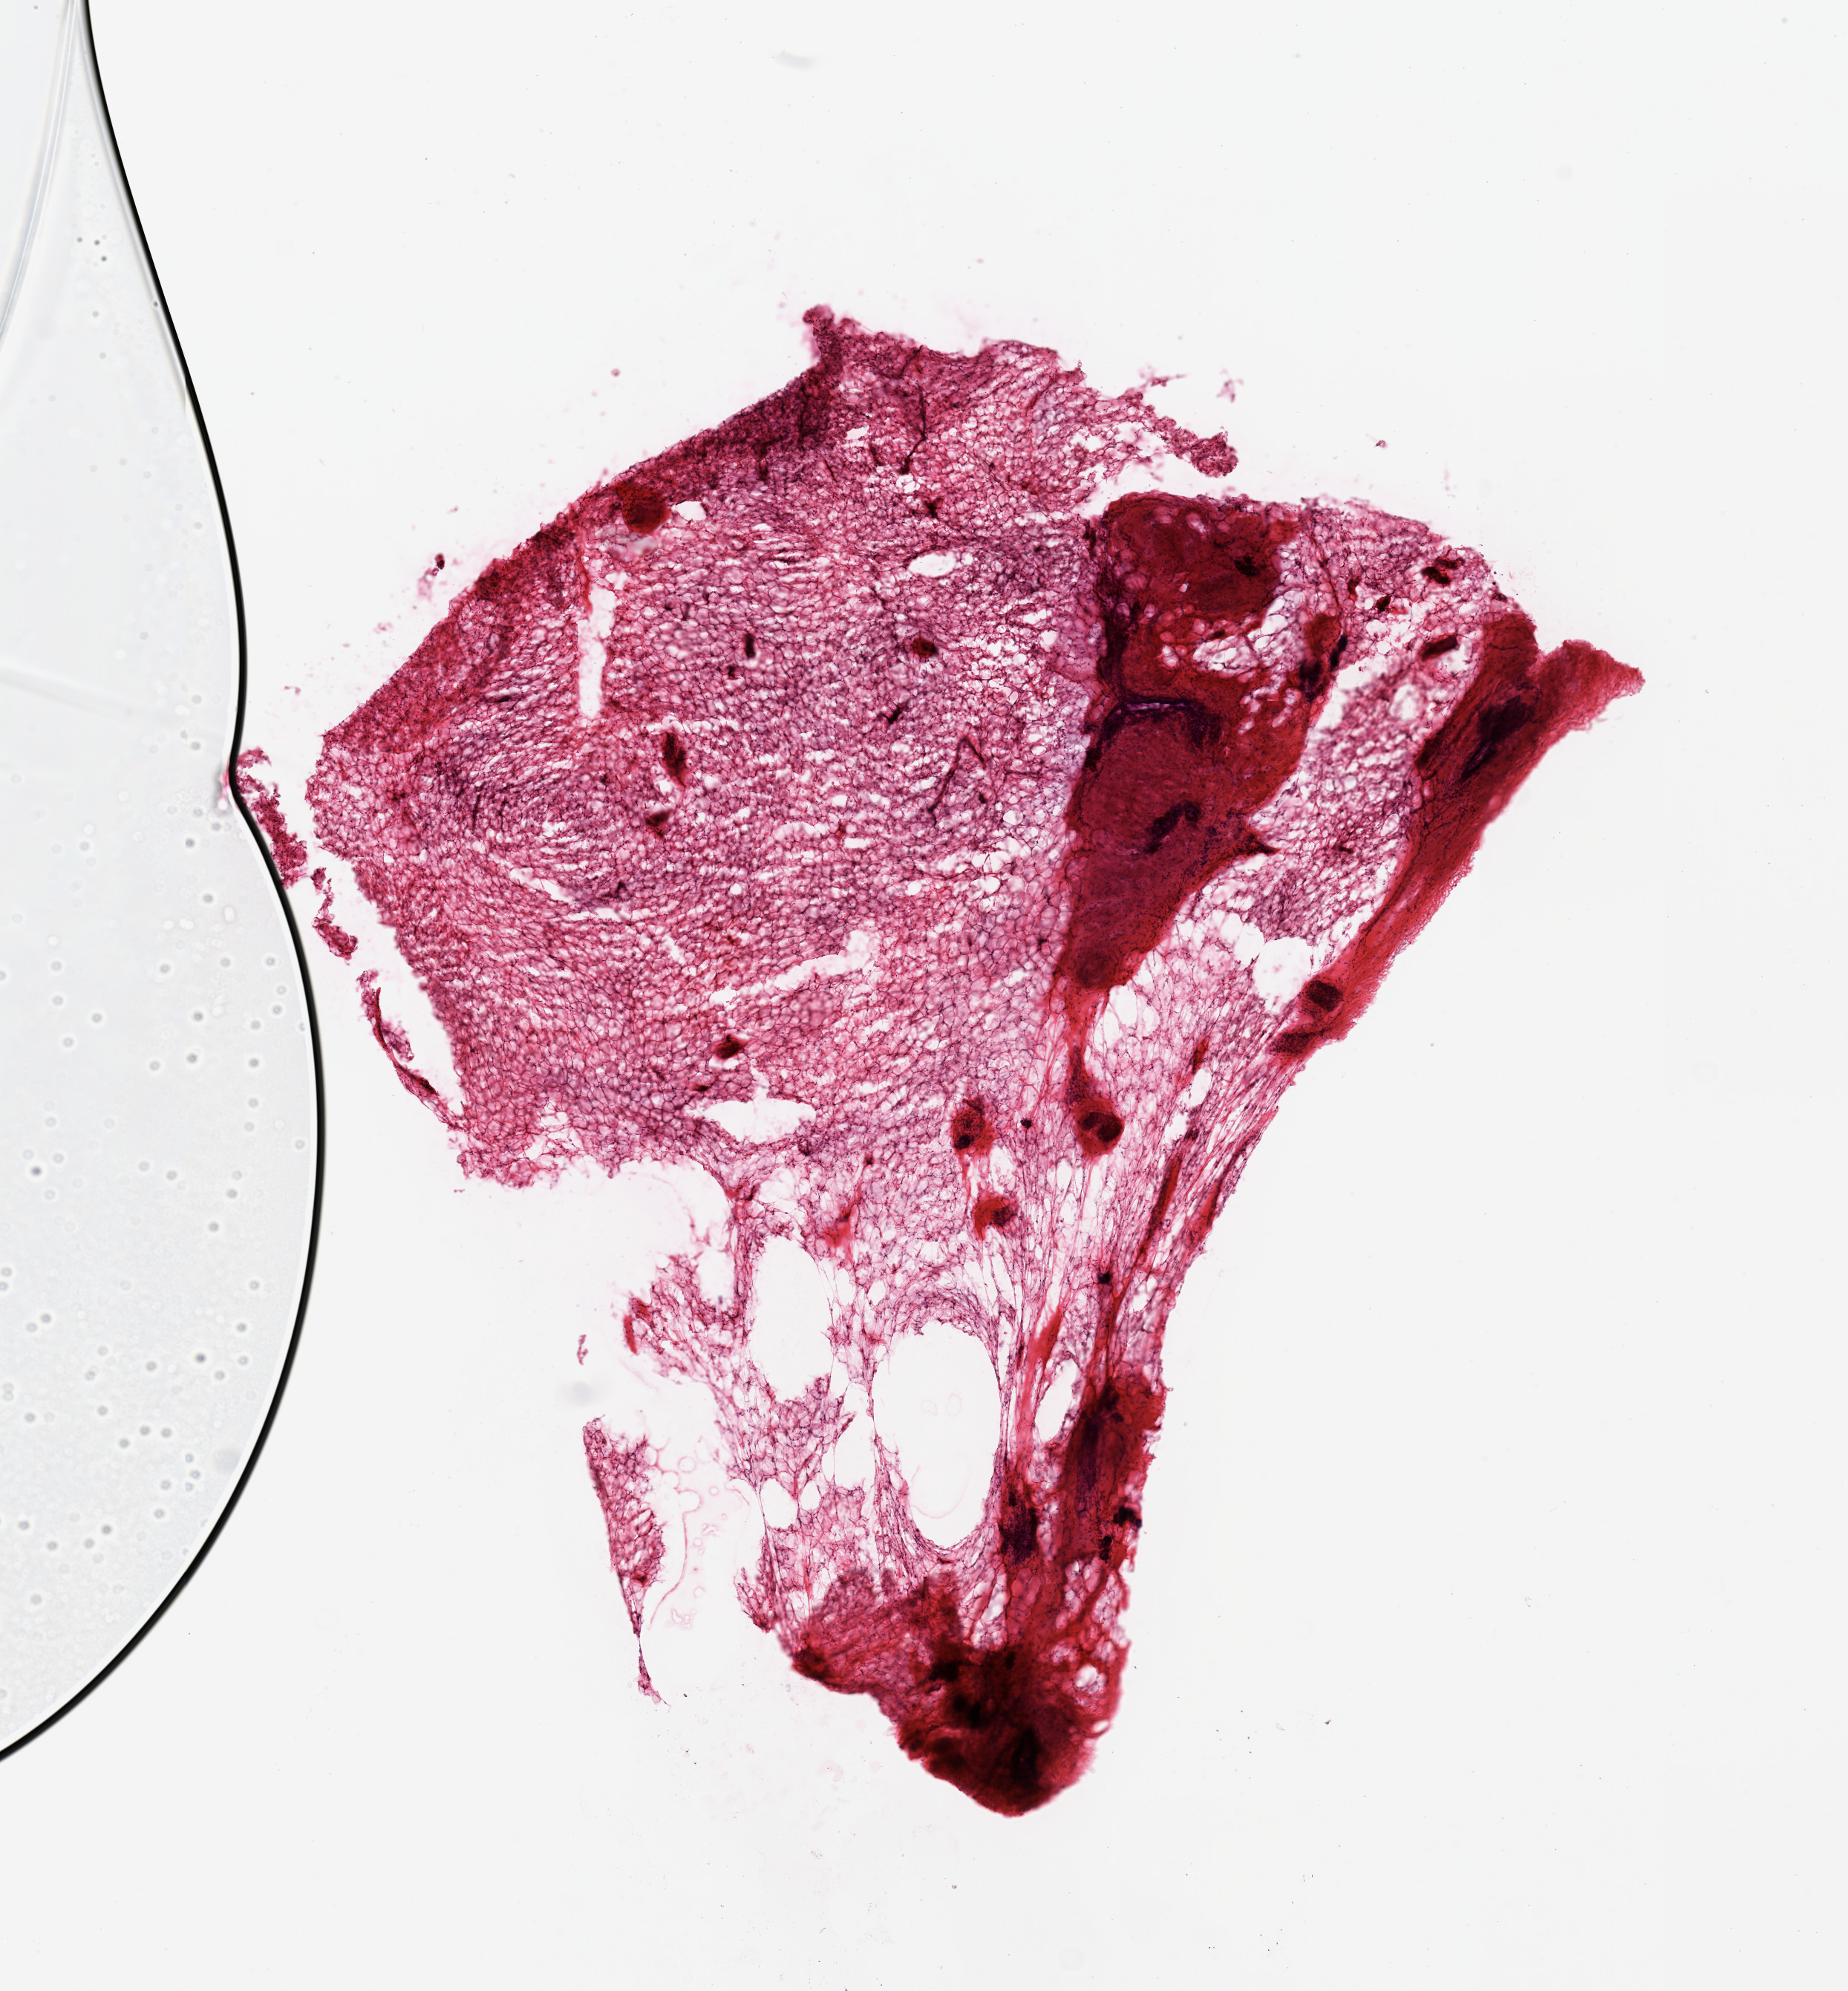
Hematoxylin and eosin (H&E) whole-slide image, a low-resolution overview of the entire scanned area, about 9.8 x 10.6 mm. Frozen section. Target tissue: breast. Donor tissue sample. Donor: female.
• review note (as recorded): 1 piece; more fibrous than fatty; ducts and lobules present